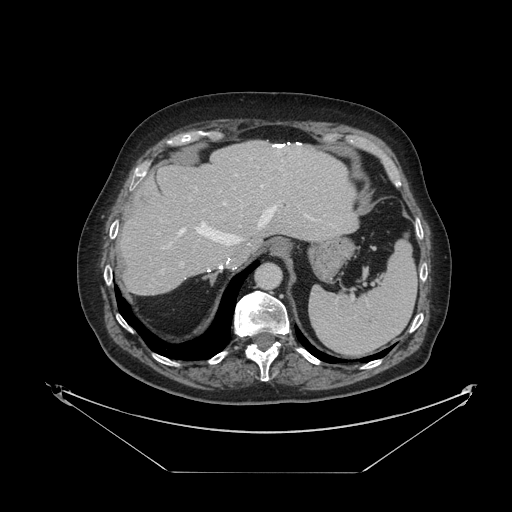
Contrast-enhanced abdominal CT, one axial slice. Position 85 of 121 along the scan axis. 120 kVp. Soft-tissue window (W 400 / L 40 HU). 2.5 mm slice thickness. 512 × 512 image matrix. Male patient, age 68 years. Case-level facts recorded for this patient, not image findings: diagnosis: colorectal cancer liver metastases, imaged before liver resection; multiple liver metastases: no; largest metastasis: 4 cm; chemotherapy before resection: yes.
Annotated regions visible in this slice (manually delineated by an expert):
- hepatic veins: bounding box (x1, y1, x2, y2) in pixels: (163, 175, 313, 249)
- liver: (120, 141, 357, 294)
- planned liver remnant (the part of the liver to remain after resection): (120, 141, 357, 295)
- portal vein (with intrahepatic branches): (180, 201, 227, 265)
- liver metastasis: (138, 193, 150, 206)